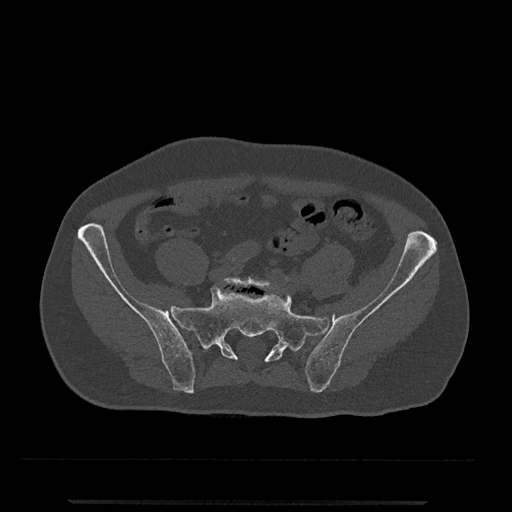
CT including the spine, one axial slice. Slice 15 of 797 in the series (ordered by position). Reconstruction kernel Br40s/3. 120 kVp. Bone window (W 1800 / L 400 HU). 0.5 mm slice thickness. 512 × 512 image matrix, field of view 419 × 419 mm. Patient: male, 63 years. From the clinical record (not read from this slice): primary cancer: prostate.
Structures marked on this image (semi-automatic segmentation, software-assisted and operator-edited):
- L5 vertebra: bounding box (x1, y1, x2, y2) in pixels: (220, 276, 273, 289)